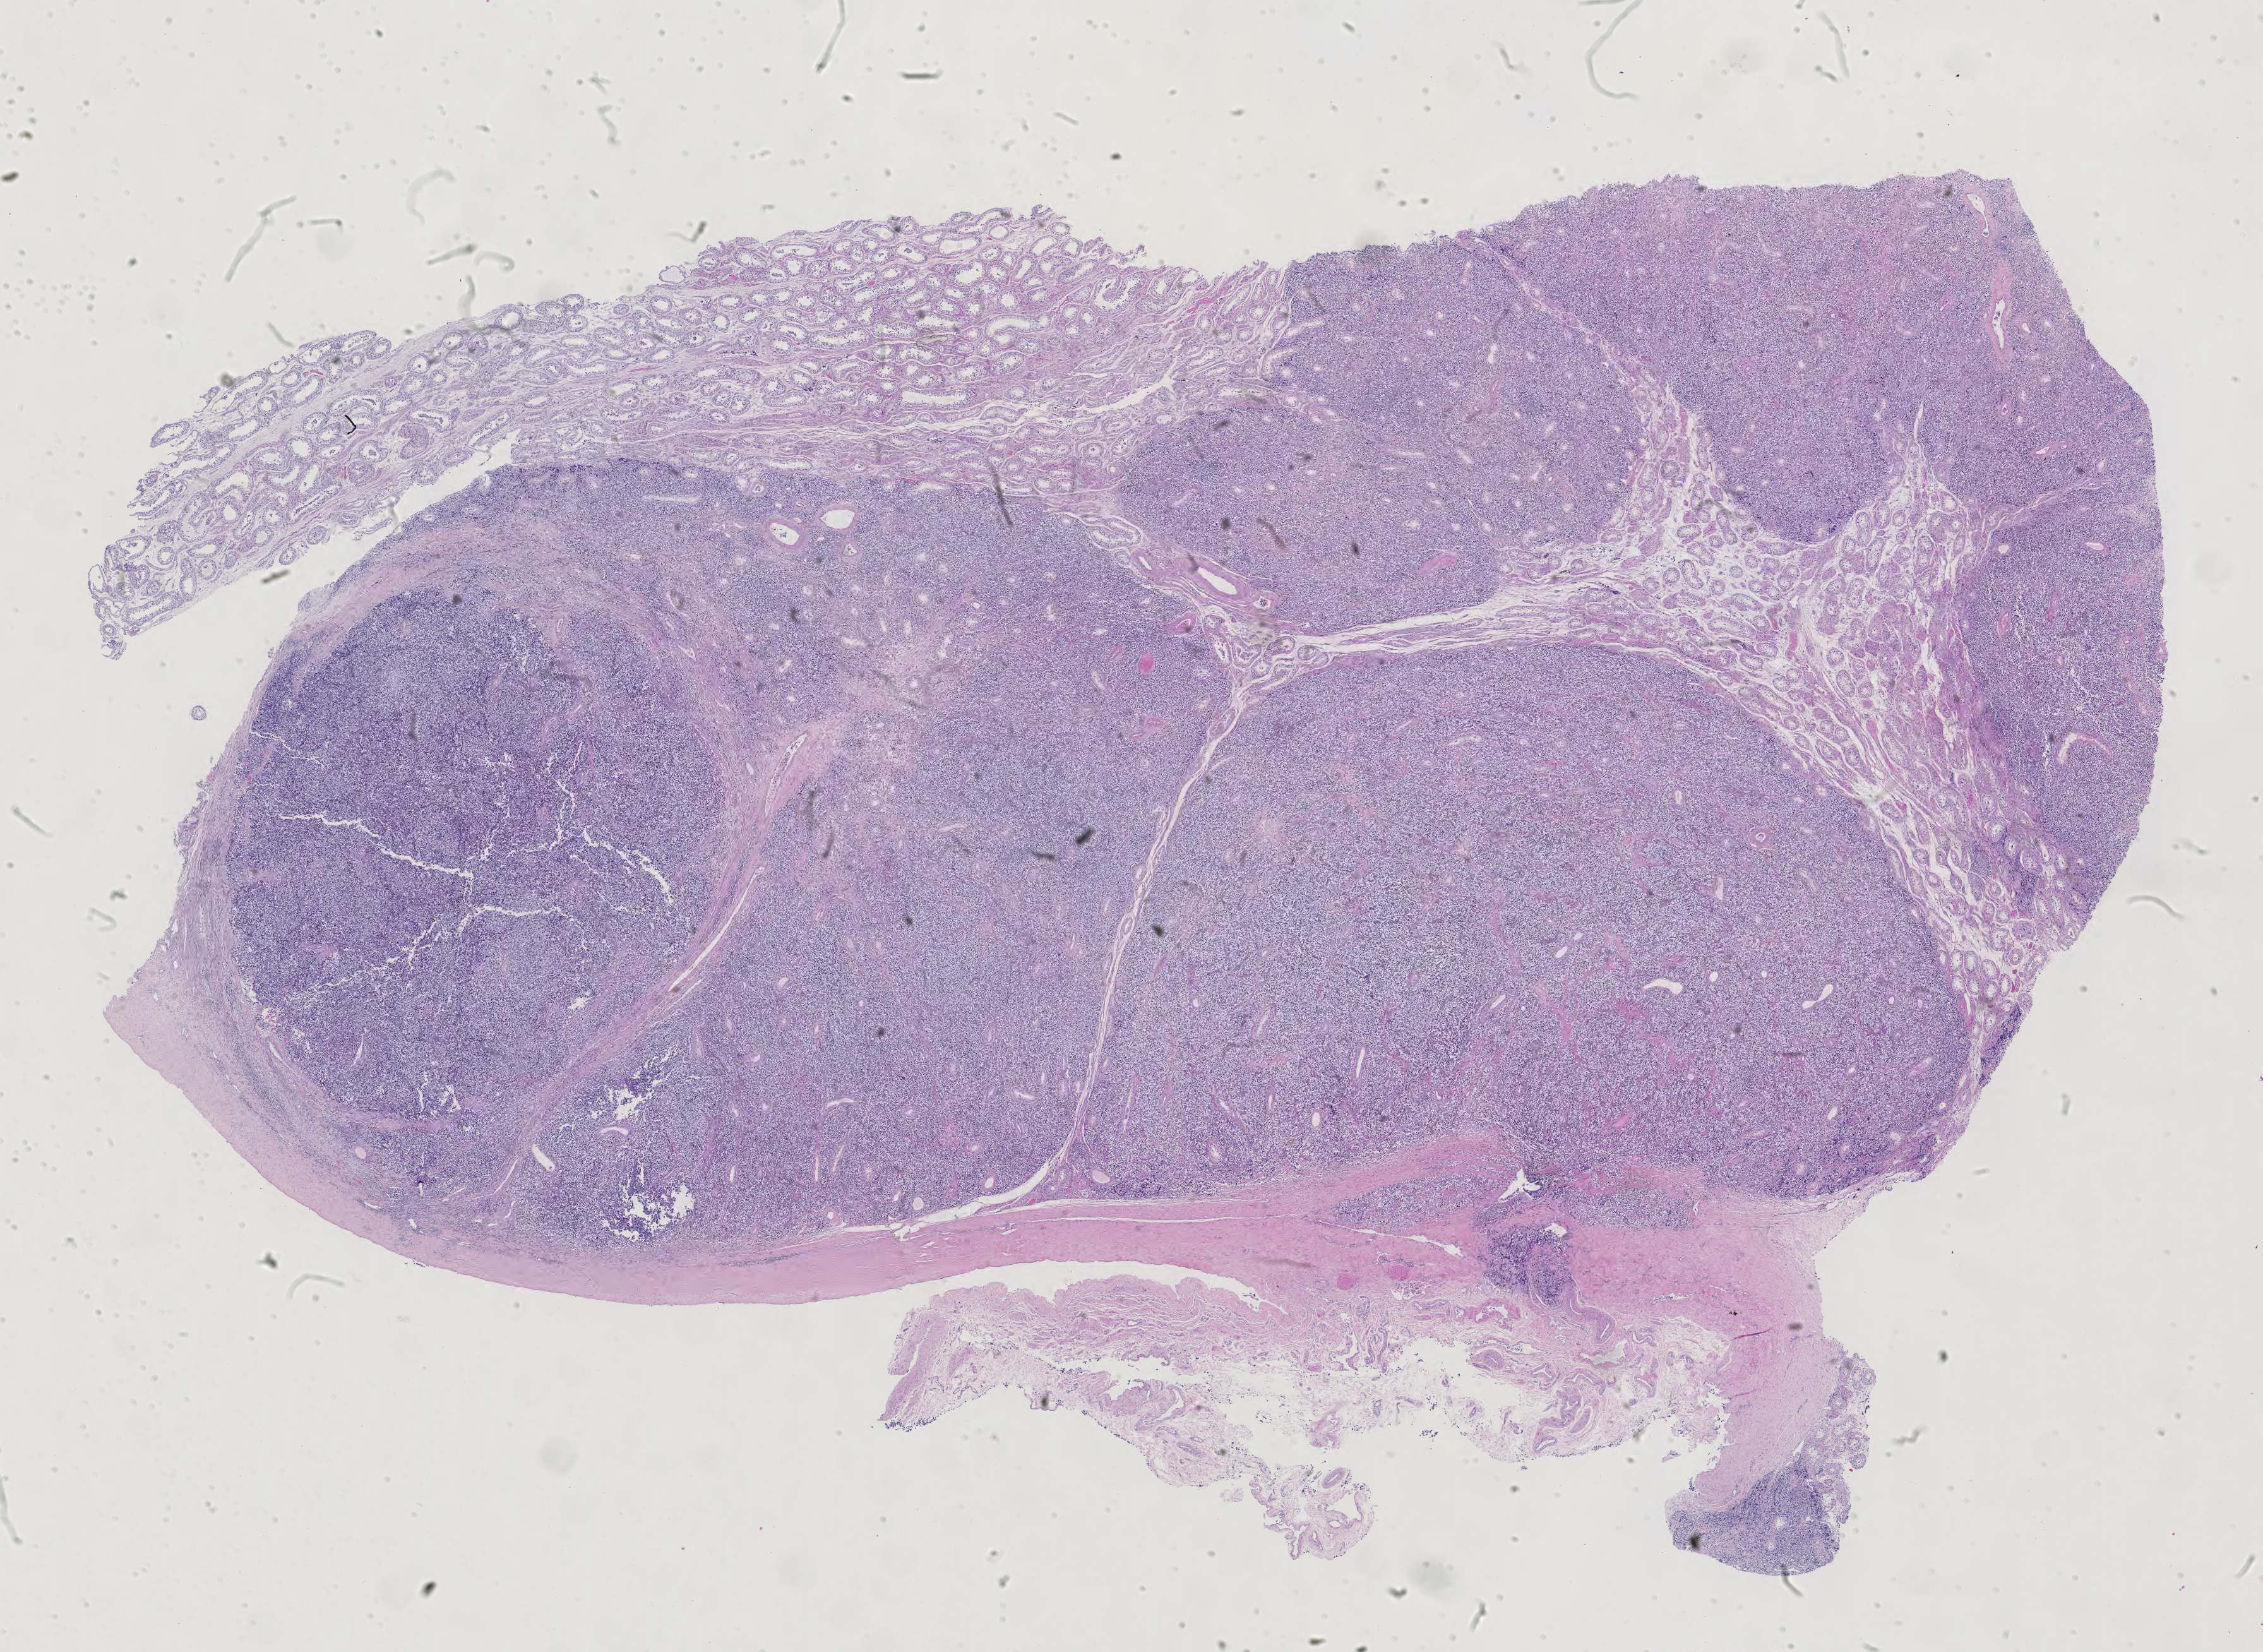
Digitized Hematoxylin and eosin (H&E) stained tissue section (whole slide) — shown as a low-resolution overview of the whole scanned area (about 26.1 x 19.1 mm), formalin-fixed paraffin-embedded (FFPE) diagnostic section, primary tumour sample from the testis. Male, age 38 years at initial diagnosis.
* diagnosis: Seminoma, NOS
* AJCC pathologic stage: IS
* TNM: T1 N0 M0